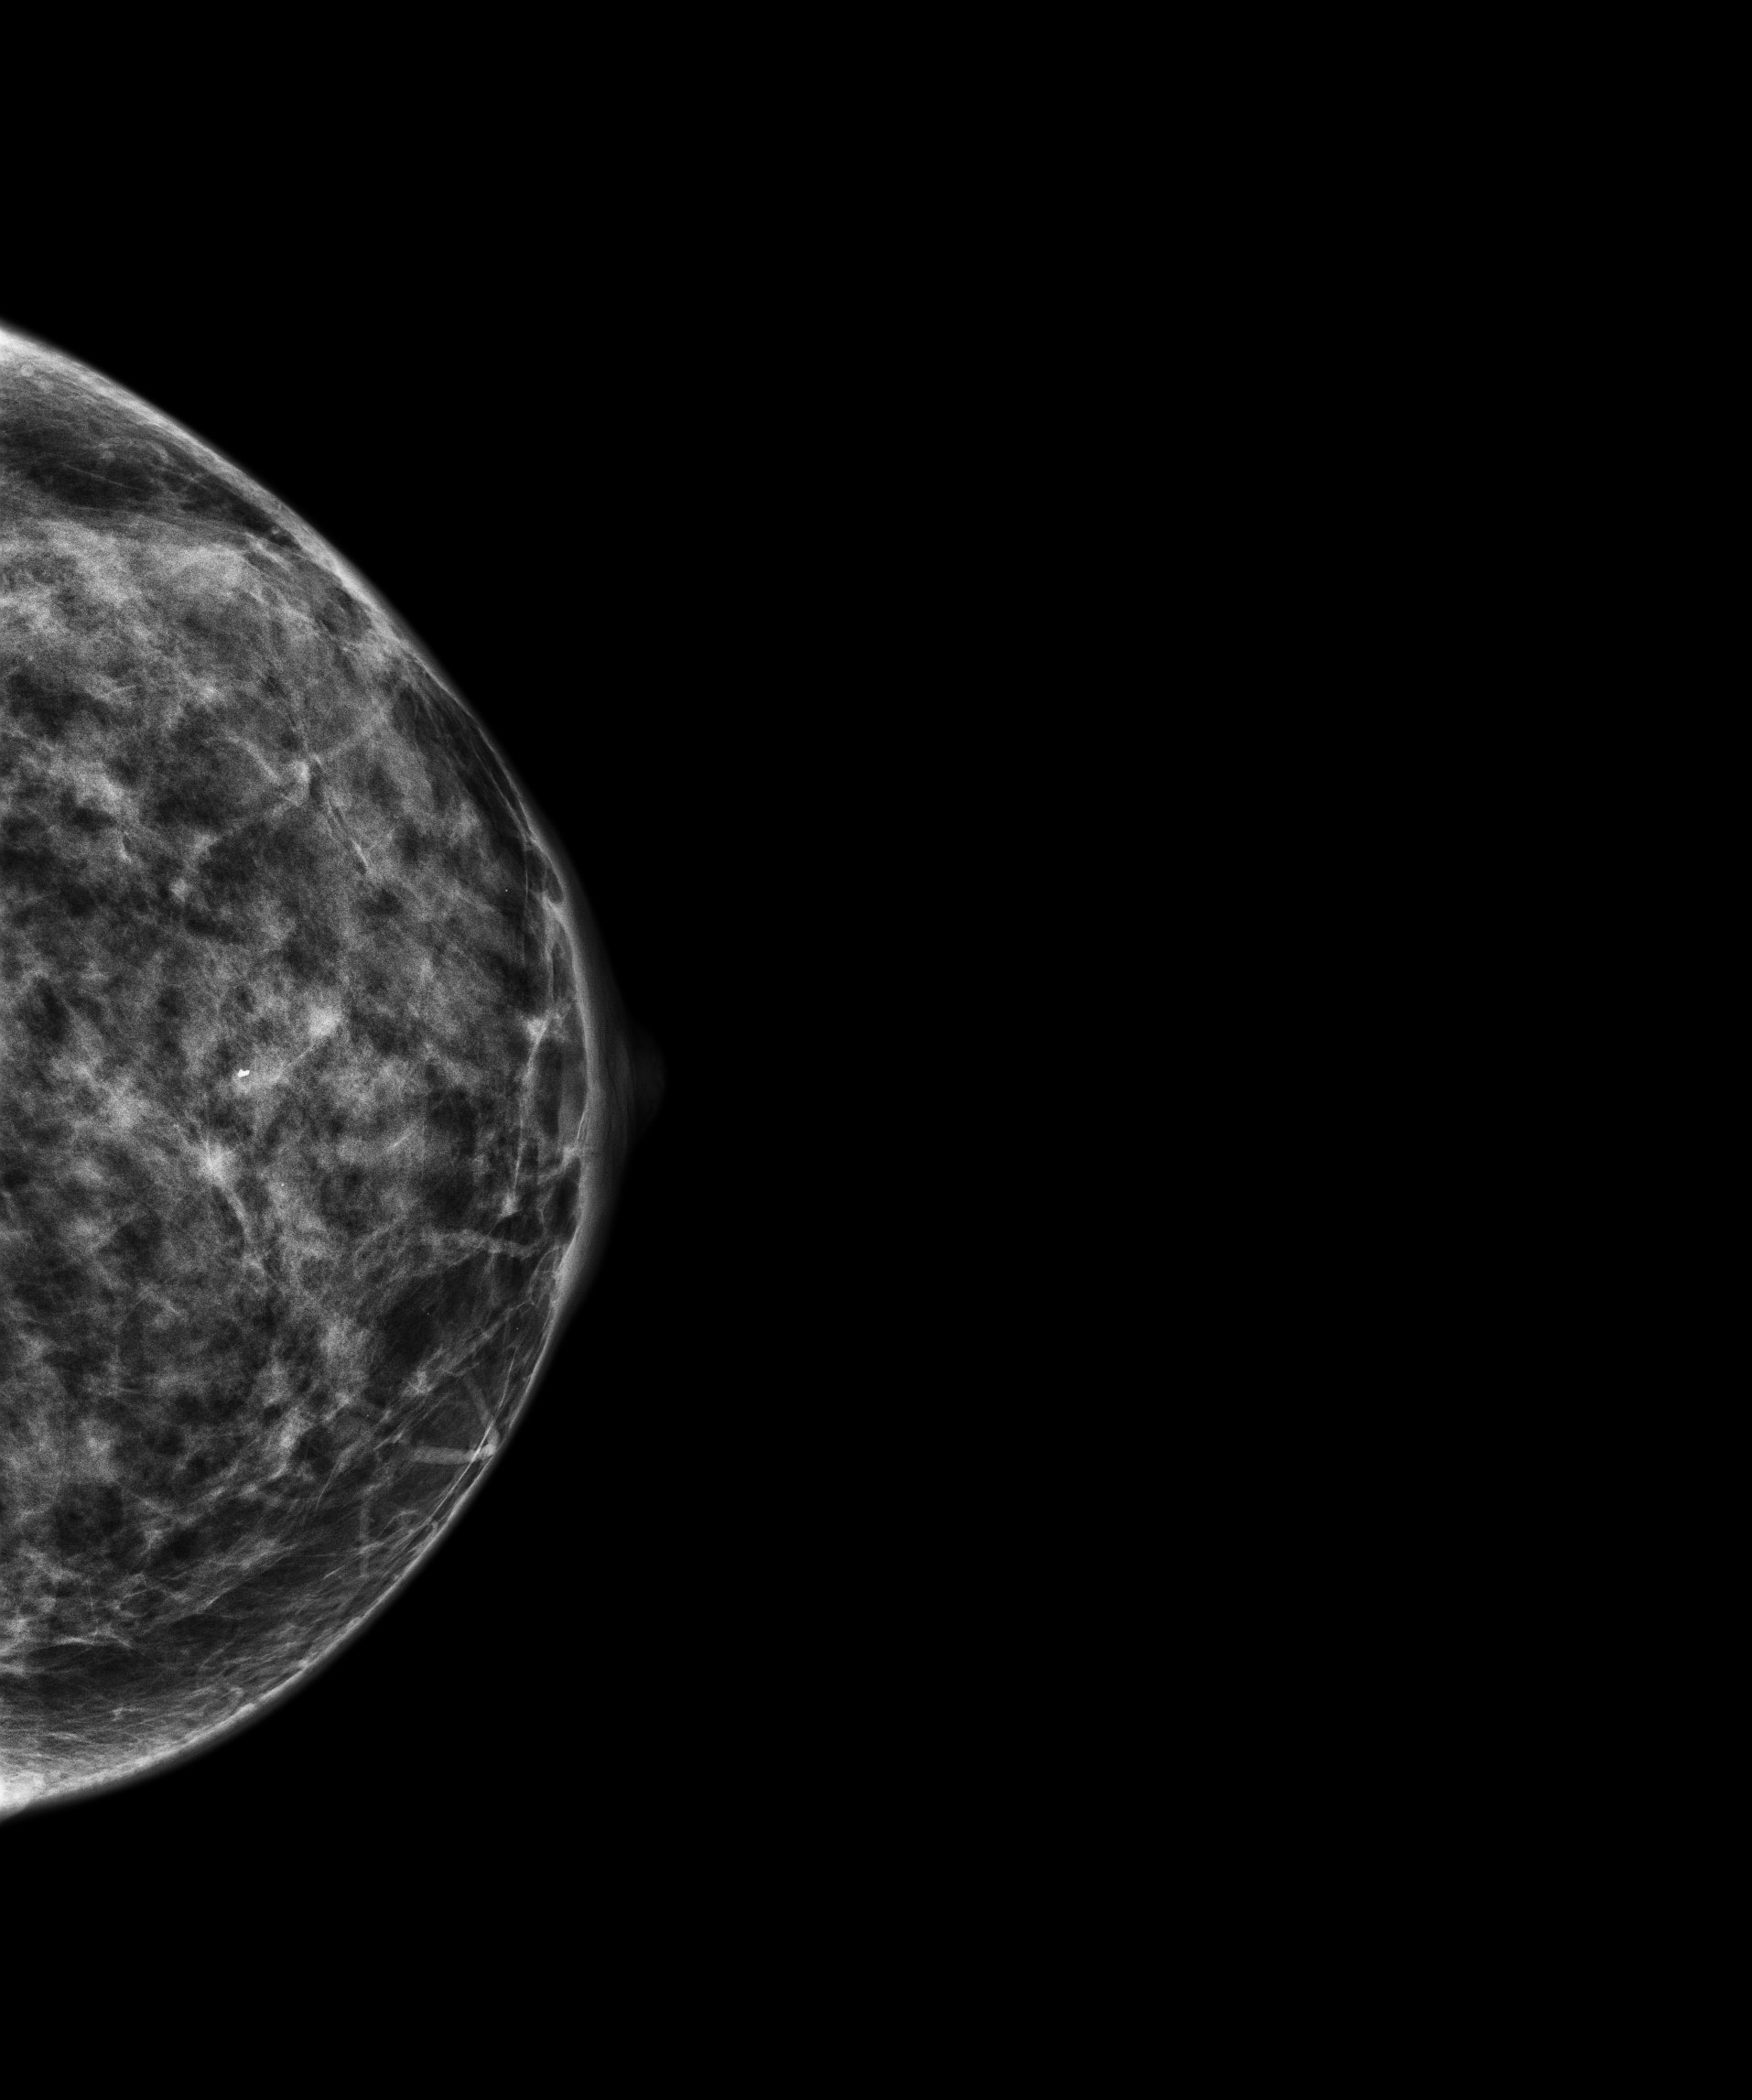
Screening examination. Patient aged 43 years (female).
Image type: full-field digital mammogram. Breast: left. Projection: CC view.